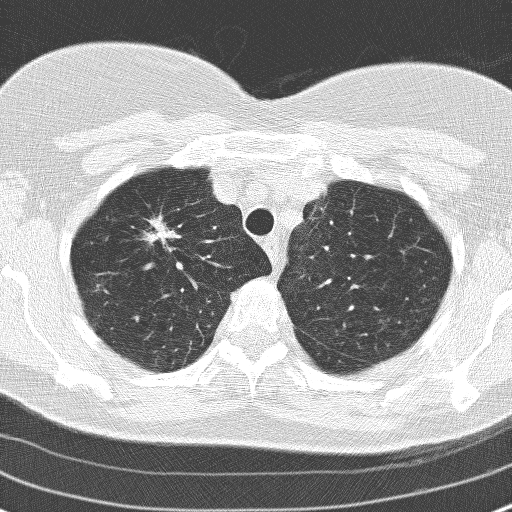
Low-dose screening chest CT, one axial slice. Position 128 of 160 along the scan axis. 120 kVp. Lung window (W 1500 / L -600 HU). 3.2 mm slice thickness. 512 × 512 image matrix, field of view 313 × 313 mm.
Annotated regions visible in this slice (expert manual segmentation):
- lesion 1 (tumor, upper lobe of right lung): bounding box <148,221,169,242> (left, top, right, bottom; pixels)